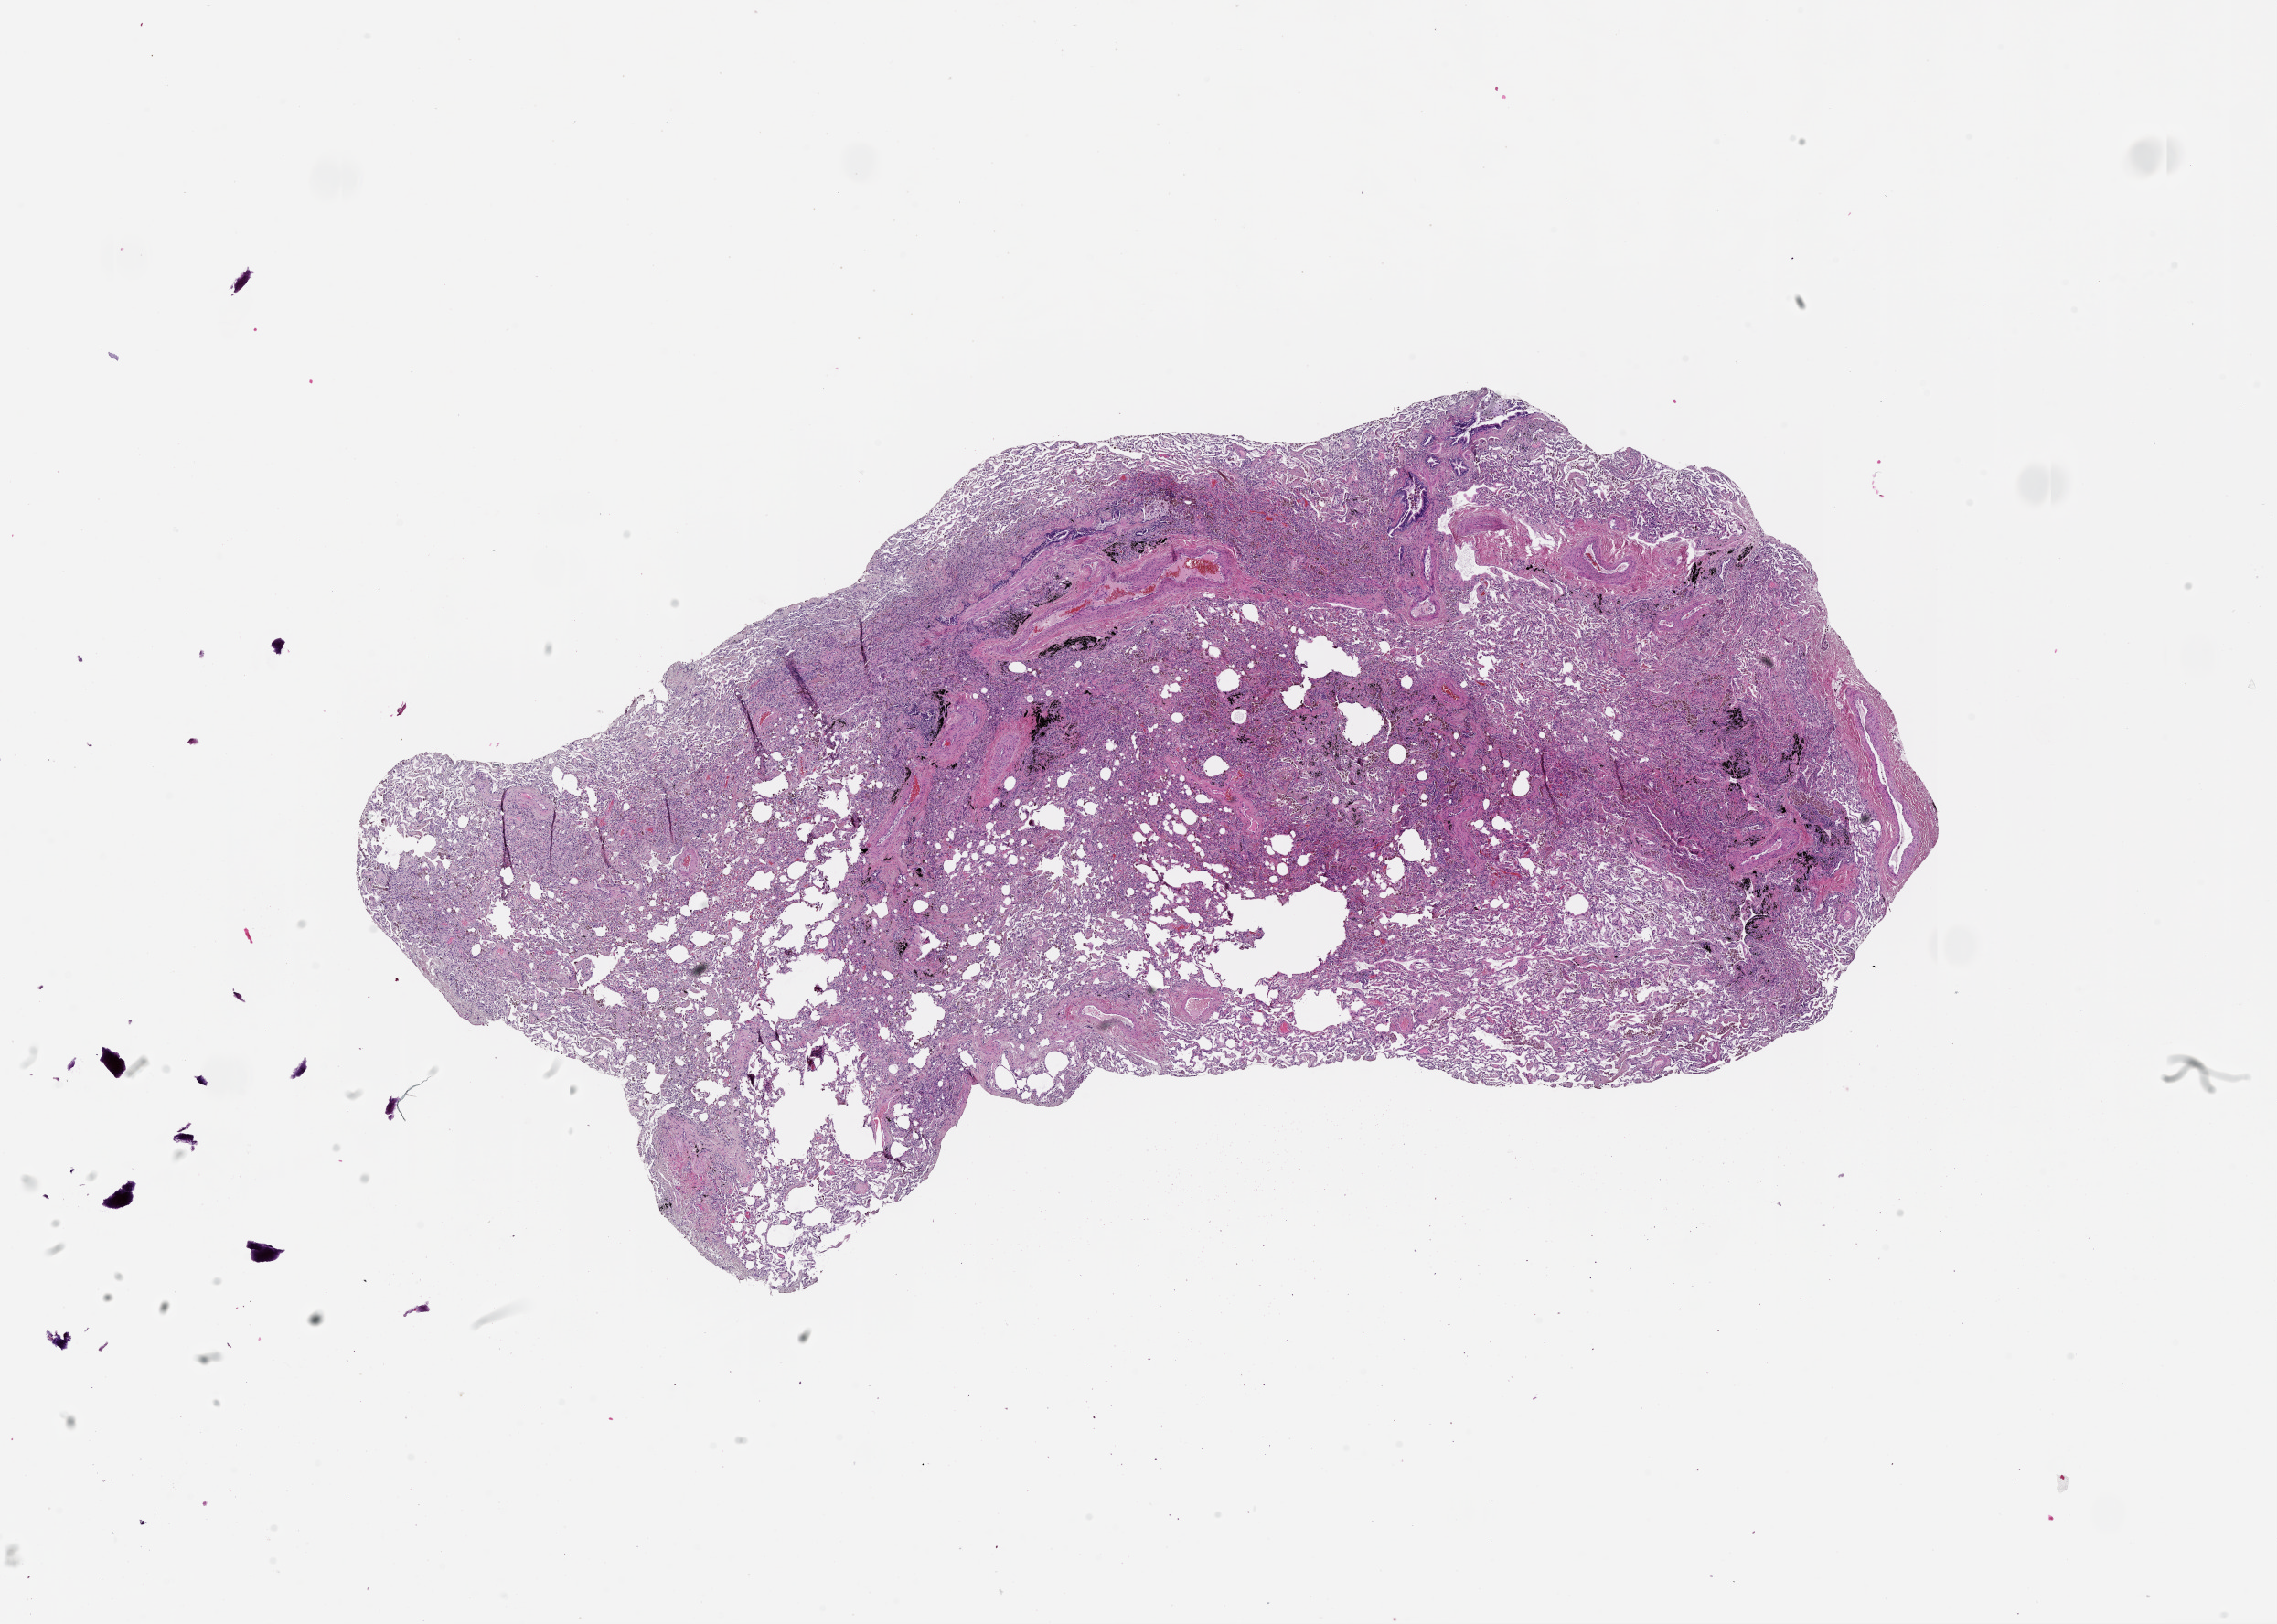
Hematoxylin and eosin (H&E) stained whole-slide image, whole scanned area (about 20.0 x 14.3 mm, acquisition: 20x scan) shown as a low-resolution overview, normal (non-tumour) tissue sample, lung. Male, 54 y/o.
This section: normal (non-tumour) tissue from the same patient. Patient diagnosis (cohort enrolment): squamous cell carcinoma (lung).